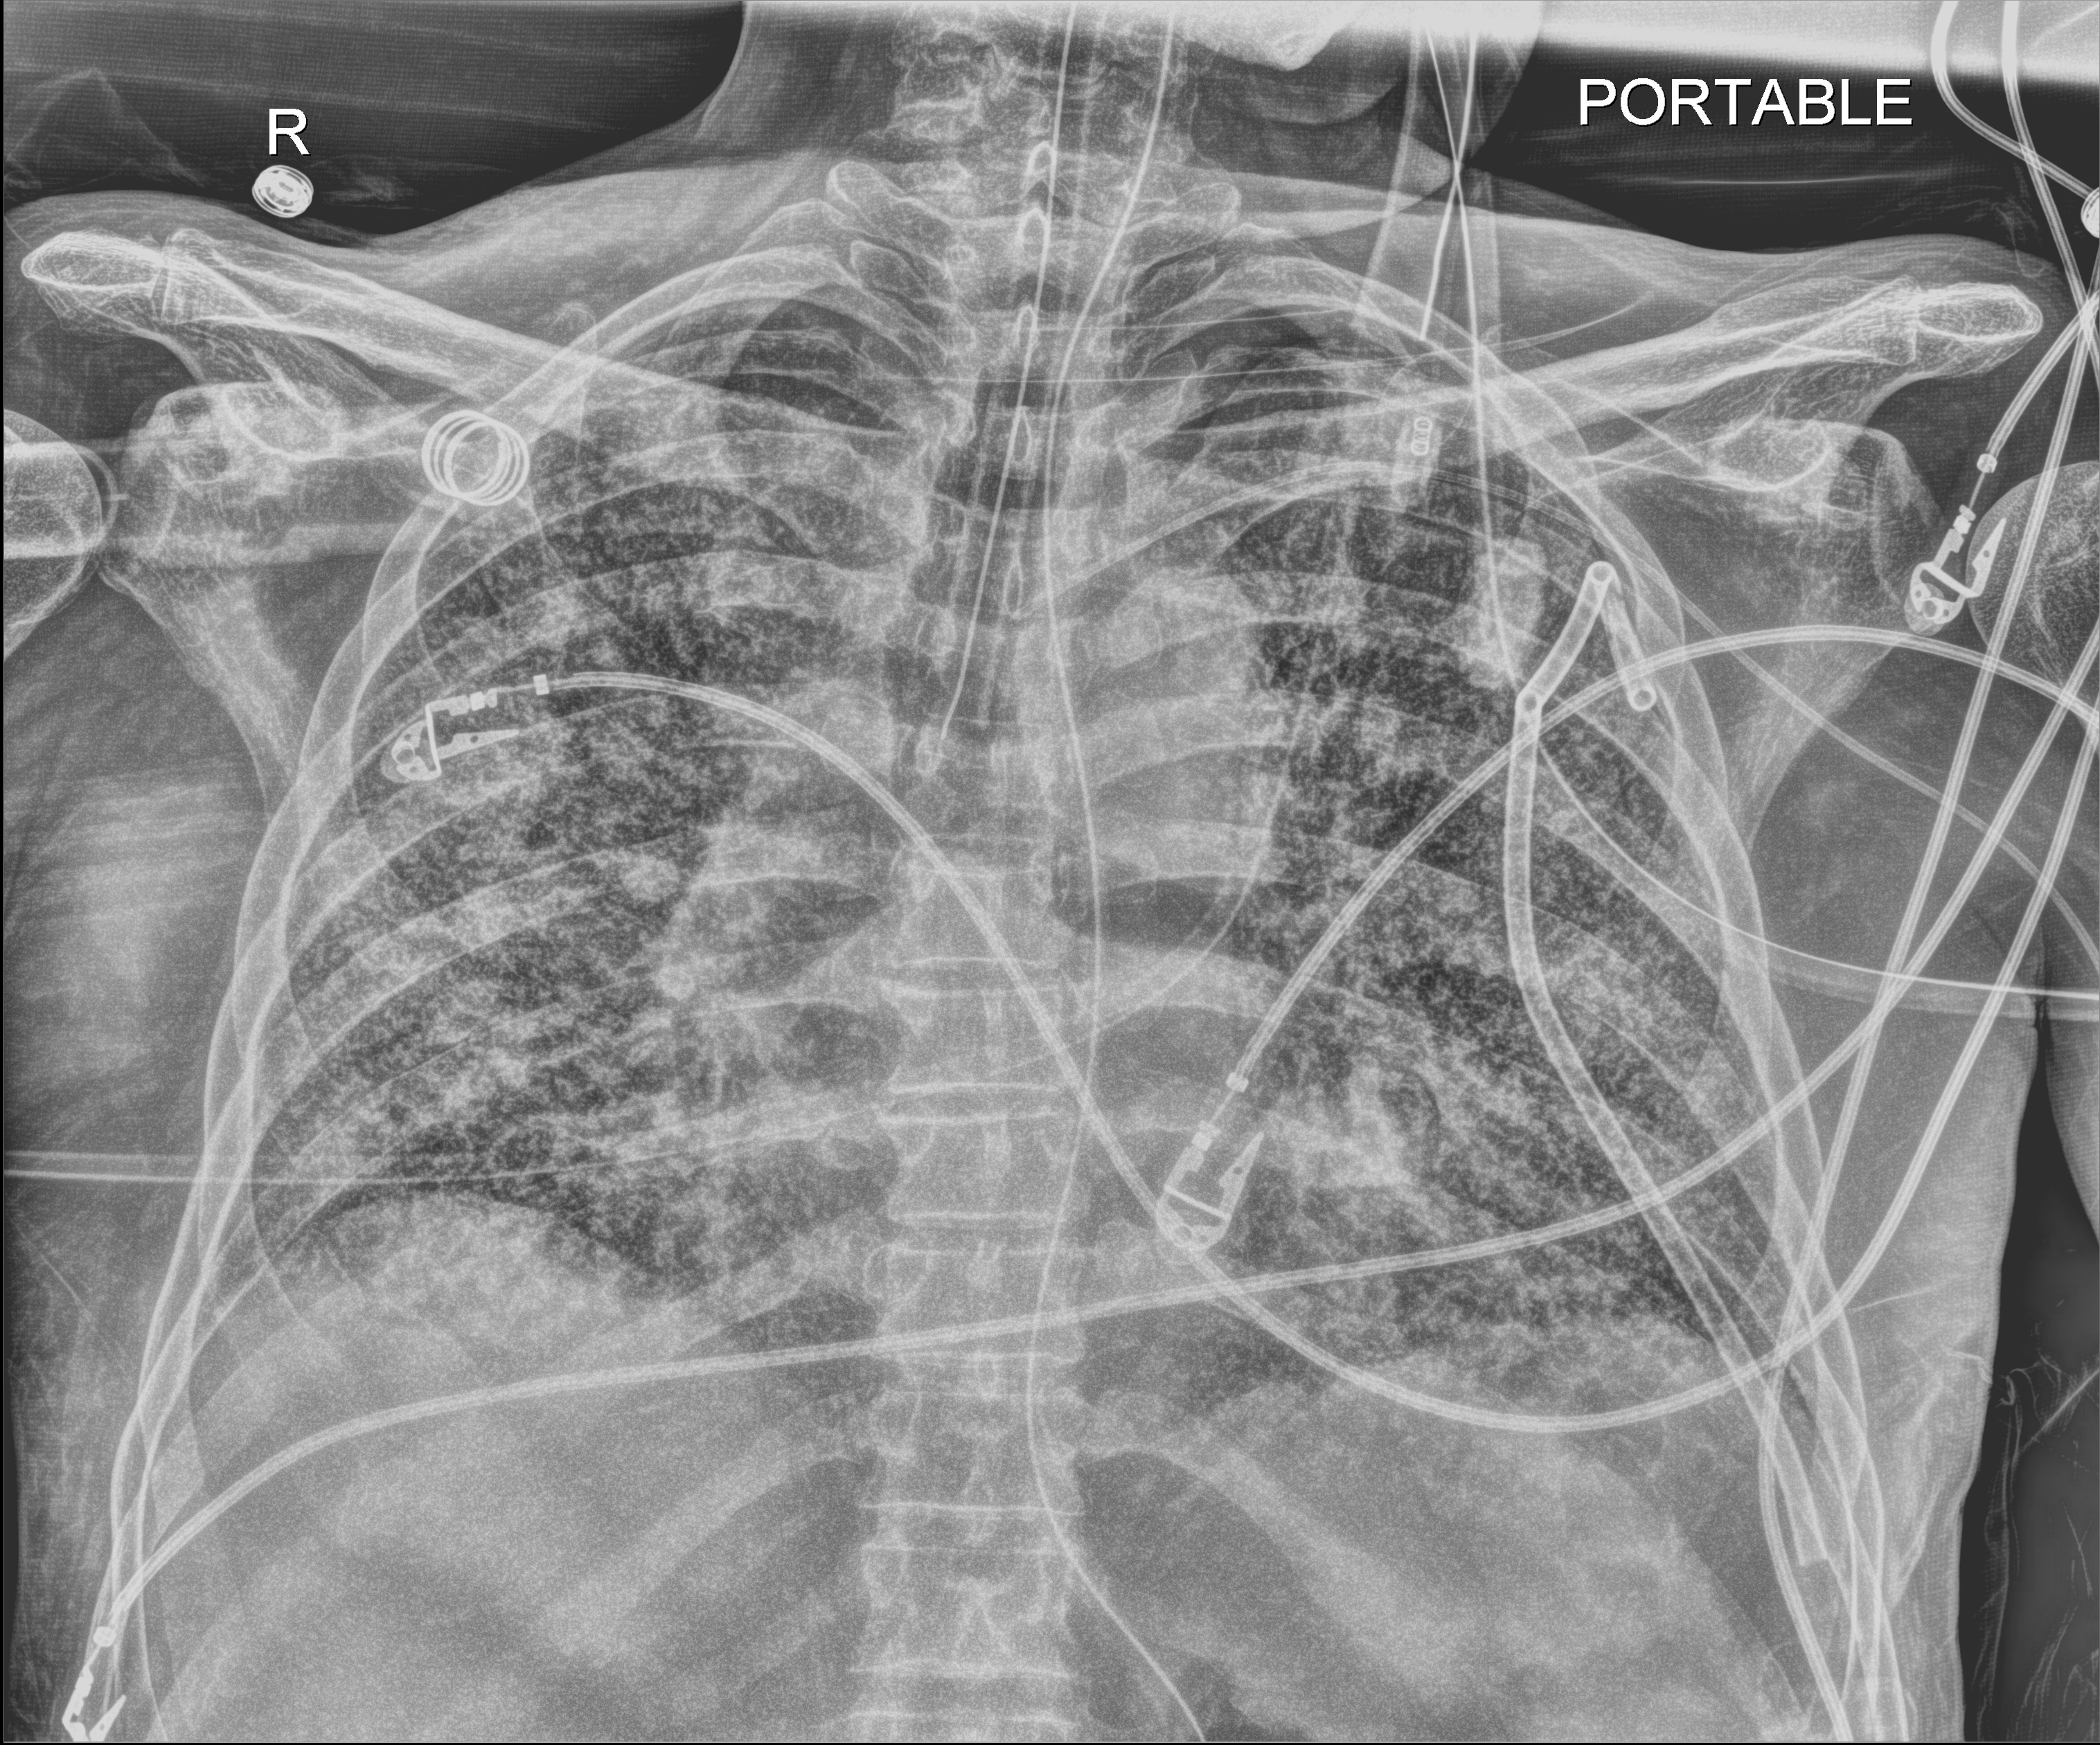
Chest radiograph (digital radiography); anteroposterior (AP) projection. Male patient hospitalised with COVID-19, age 60–74 years.
Admission-level facts for this patient (not findings on this image; timing relative to this image not recorded):
- length of hospital stay: 54 days
- mechanically ventilated during this hospital stay: yes